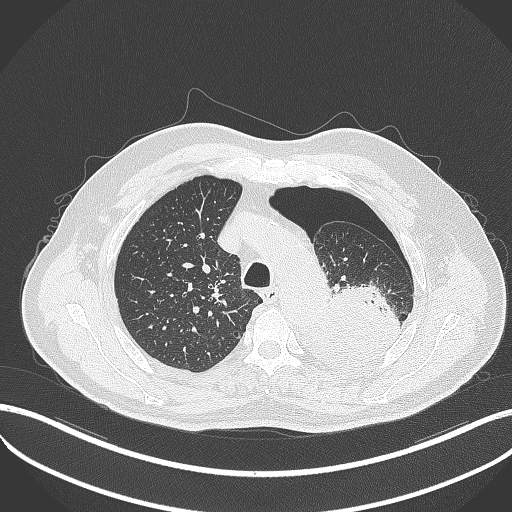
Chest CT, one axial slice. Slice 386 of 464 in the series (ordered by position). 120 kVp. Lung window (W 1500 / L -600 HU). 1 mm slice thickness. 512 × 512 image matrix. Patient: male, 76 years. From the clinical record (not read from this slice): clinical TNM (as recorded): T3 N0 M1b.
Structures marked on this image (rectangle marked by the reading radiologist):
- lung tumour (recorded histology: adenocarcinoma): box from (x=297, y=283) to (x=405, y=378) px